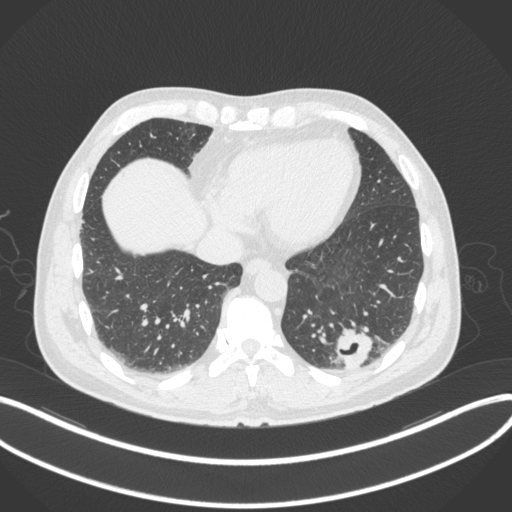
Chest CT, one axial slice; reconstruction kernel B31f; 120 kVp; lung window (W 1500 / L -600 HU); 1 mm slice thickness; 512 × 512 image matrix, field of view 400 × 400 mm. Male patient, age 54 years. From the clinical record (not read from this slice): clinical TNM (as recorded): T1c N0 M1.
Structures marked on this image (rectangle marked by the reading radiologist):
- lung tumour (recorded histology: adenocarcinoma): bounding box (x1, y1, x2, y2) in pixels: (330, 323, 376, 371)